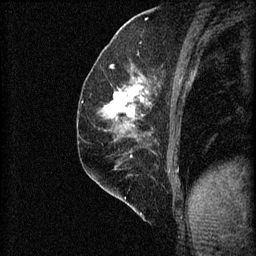
Breast MRI (dynamic contrast-enhanced), one sagittal slice. Slice 29 of 60 in the series (ordered by position). 3 images stored at this slice position (order not interpretable as contrast timing). 1.5 T. TE 4.2 ms, TR 8.2 ms. 2 mm slice thickness. 256 × 256 image matrix, field of view 180 × 180 mm. Female patient, age 59 years.
Outlined on this slice (semi-automatically segmented with operator editing):
- analysis volume of interest (the breast-tissue region the enhancement analysis was run in; not a lesion): bounding box [x1, y1, x2, y2] px = [100, 74, 154, 131]
- tumour enhancement mask (voxels above the 70 % enhancement threshold inside the analysis volume of interest): [103, 84, 152, 127]